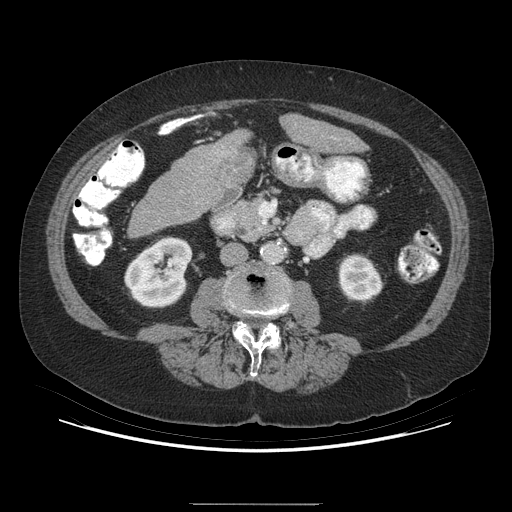
Contrast-enhanced abdominal CT (liver protocol), one axial slice. Position 128 of 192 along the scan axis. Reconstruction kernel STANDARD. 140 kVp. Soft-tissue window (W 400 / L 40 HU). 2.5 mm slice thickness. 512 × 512 image matrix, field of view 400 × 400 mm. Case-level facts recorded for this patient, not image findings: diagnosis: hepatocellular carcinoma (patient treated with transarterial chemoembolisation; whether this scan precedes or follows treatment is not stated here); TNM stage (as recorded): Stage-I; Child-Pugh class: A; tumour differentiation: moderately differentiated; tumour nodularity: uninodular.
Annotated regions visible in this slice (semi-automatic segmentation, software-assisted and operator-edited):
- liver parenchyma outside the tumour (the mass and vessels are separate outlines, so this box may not span the whole liver): bounding box <288,118,358,148> (left, top, right, bottom; pixels)
- mass: <218,147,254,186>